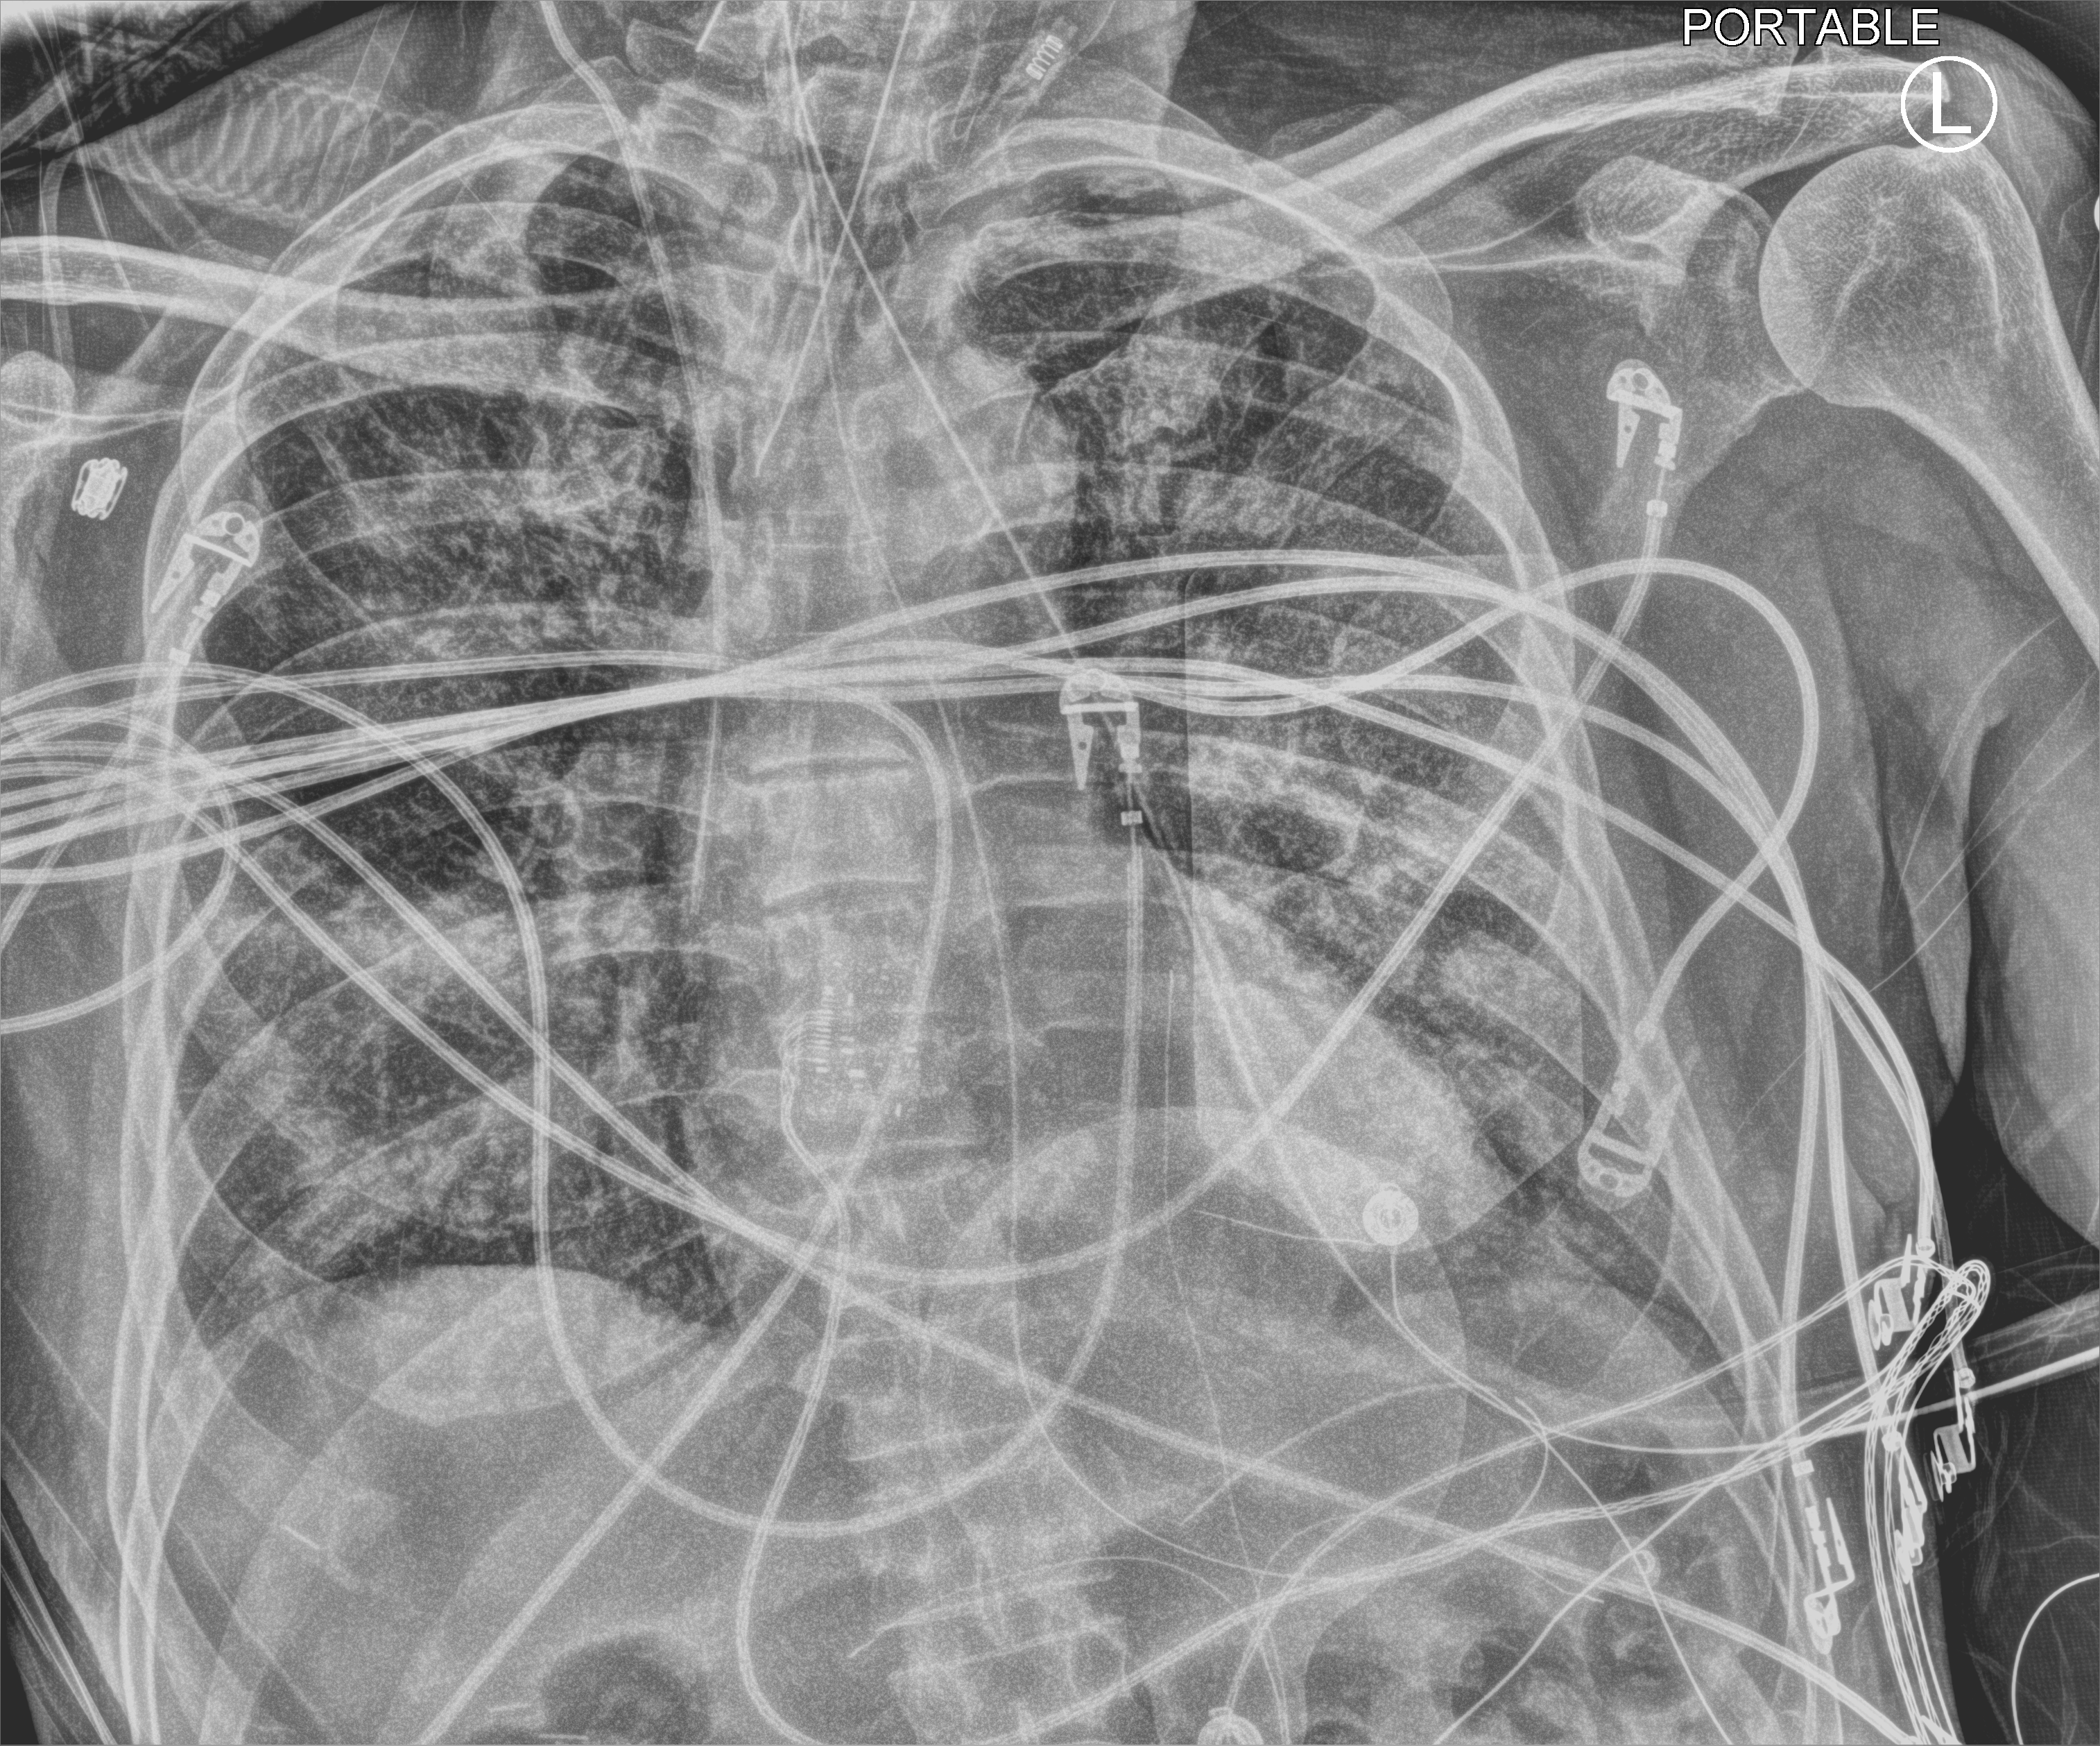
Portable chest radiograph; anteroposterior (AP) projection. Male patient hospitalised with COVID-19, age 60–74 years.
From the hospital-stay record, not from the radiograph (when in the stay this image was taken is not recorded): length of hospital stay: 31 days; mechanically ventilated during this hospital stay: yes.